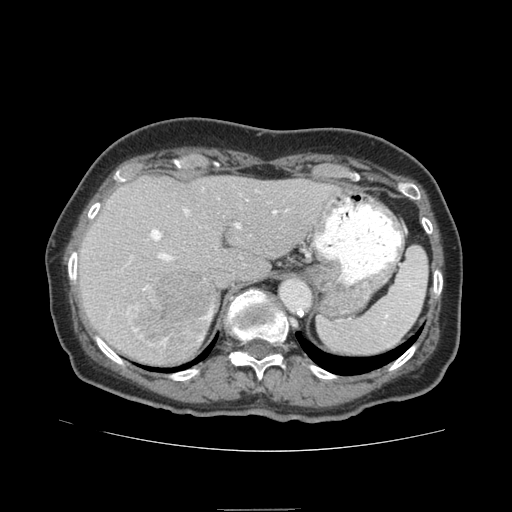
Contrast-enhanced abdominal CT (liver protocol), one axial slice. Slice 58 of 95 in the series (ordered by position). Reconstruction kernel STANDARD. Soft-tissue window (W 400 / L 40 HU). 2.5 mm slice thickness. 512 × 512 image matrix. Case-level facts recorded for this patient, not image findings: diagnosis: hepatocellular carcinoma (patient treated with transarterial chemoembolisation; whether this scan precedes or follows treatment is not stated here); TNM stage (as recorded): Stage-IVA; Child-Pugh class: B.
Structures marked on this image (semi-automatic segmentation, software-assisted and operator-edited):
- liver parenchyma outside the tumour (the mass and vessels are separate outlines, so this box may not span the whole liver): bounding box (x1, y1, x2, y2) in pixels: (78, 176, 340, 364)
- mass: (129, 270, 217, 357)
- liver vessels: (127, 209, 277, 341)